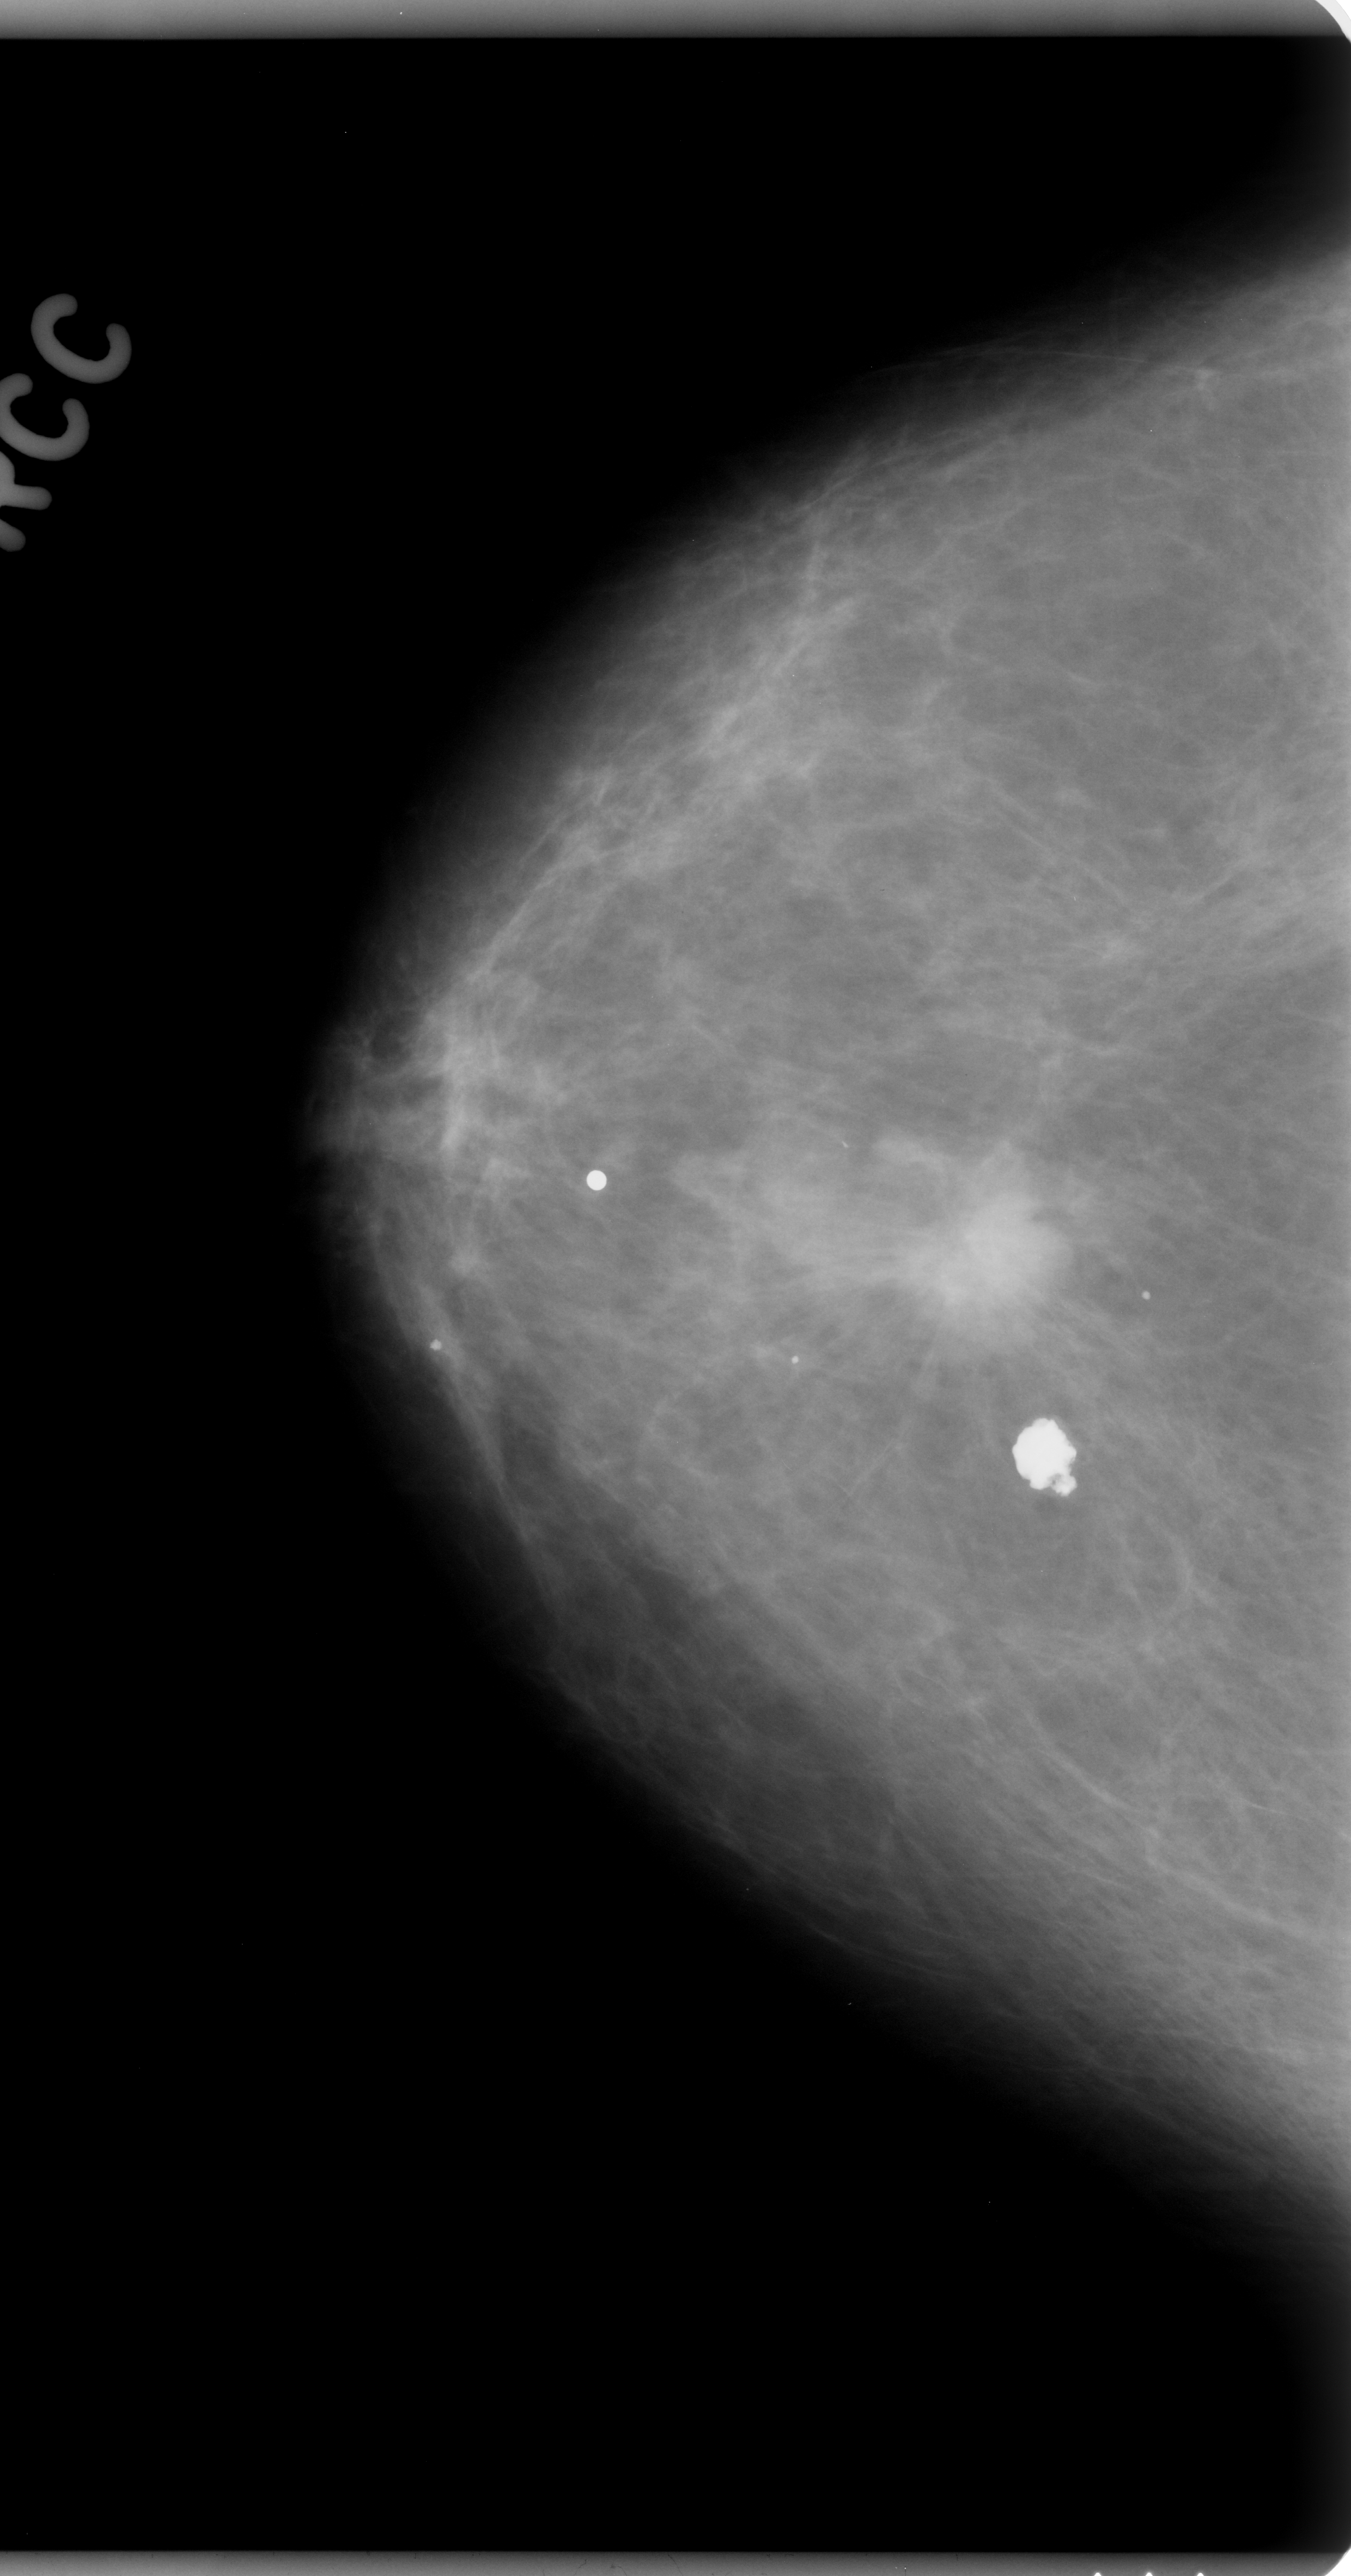
Mammogram (digitized film); right breast; CC view; breast composition: almost entirely fatty (BI-RADS density category 1 of 4); 1351 × 2576 image matrix.
Expert-marked regions of interest on this image (one box per marked abnormality):
- mass, shape irregular, margins spiculated; BI-RADS assessment category 5; pathology (as recorded): malignant: bounding box [x1, y1, x2, y2] px = [872, 1150, 1074, 1357]